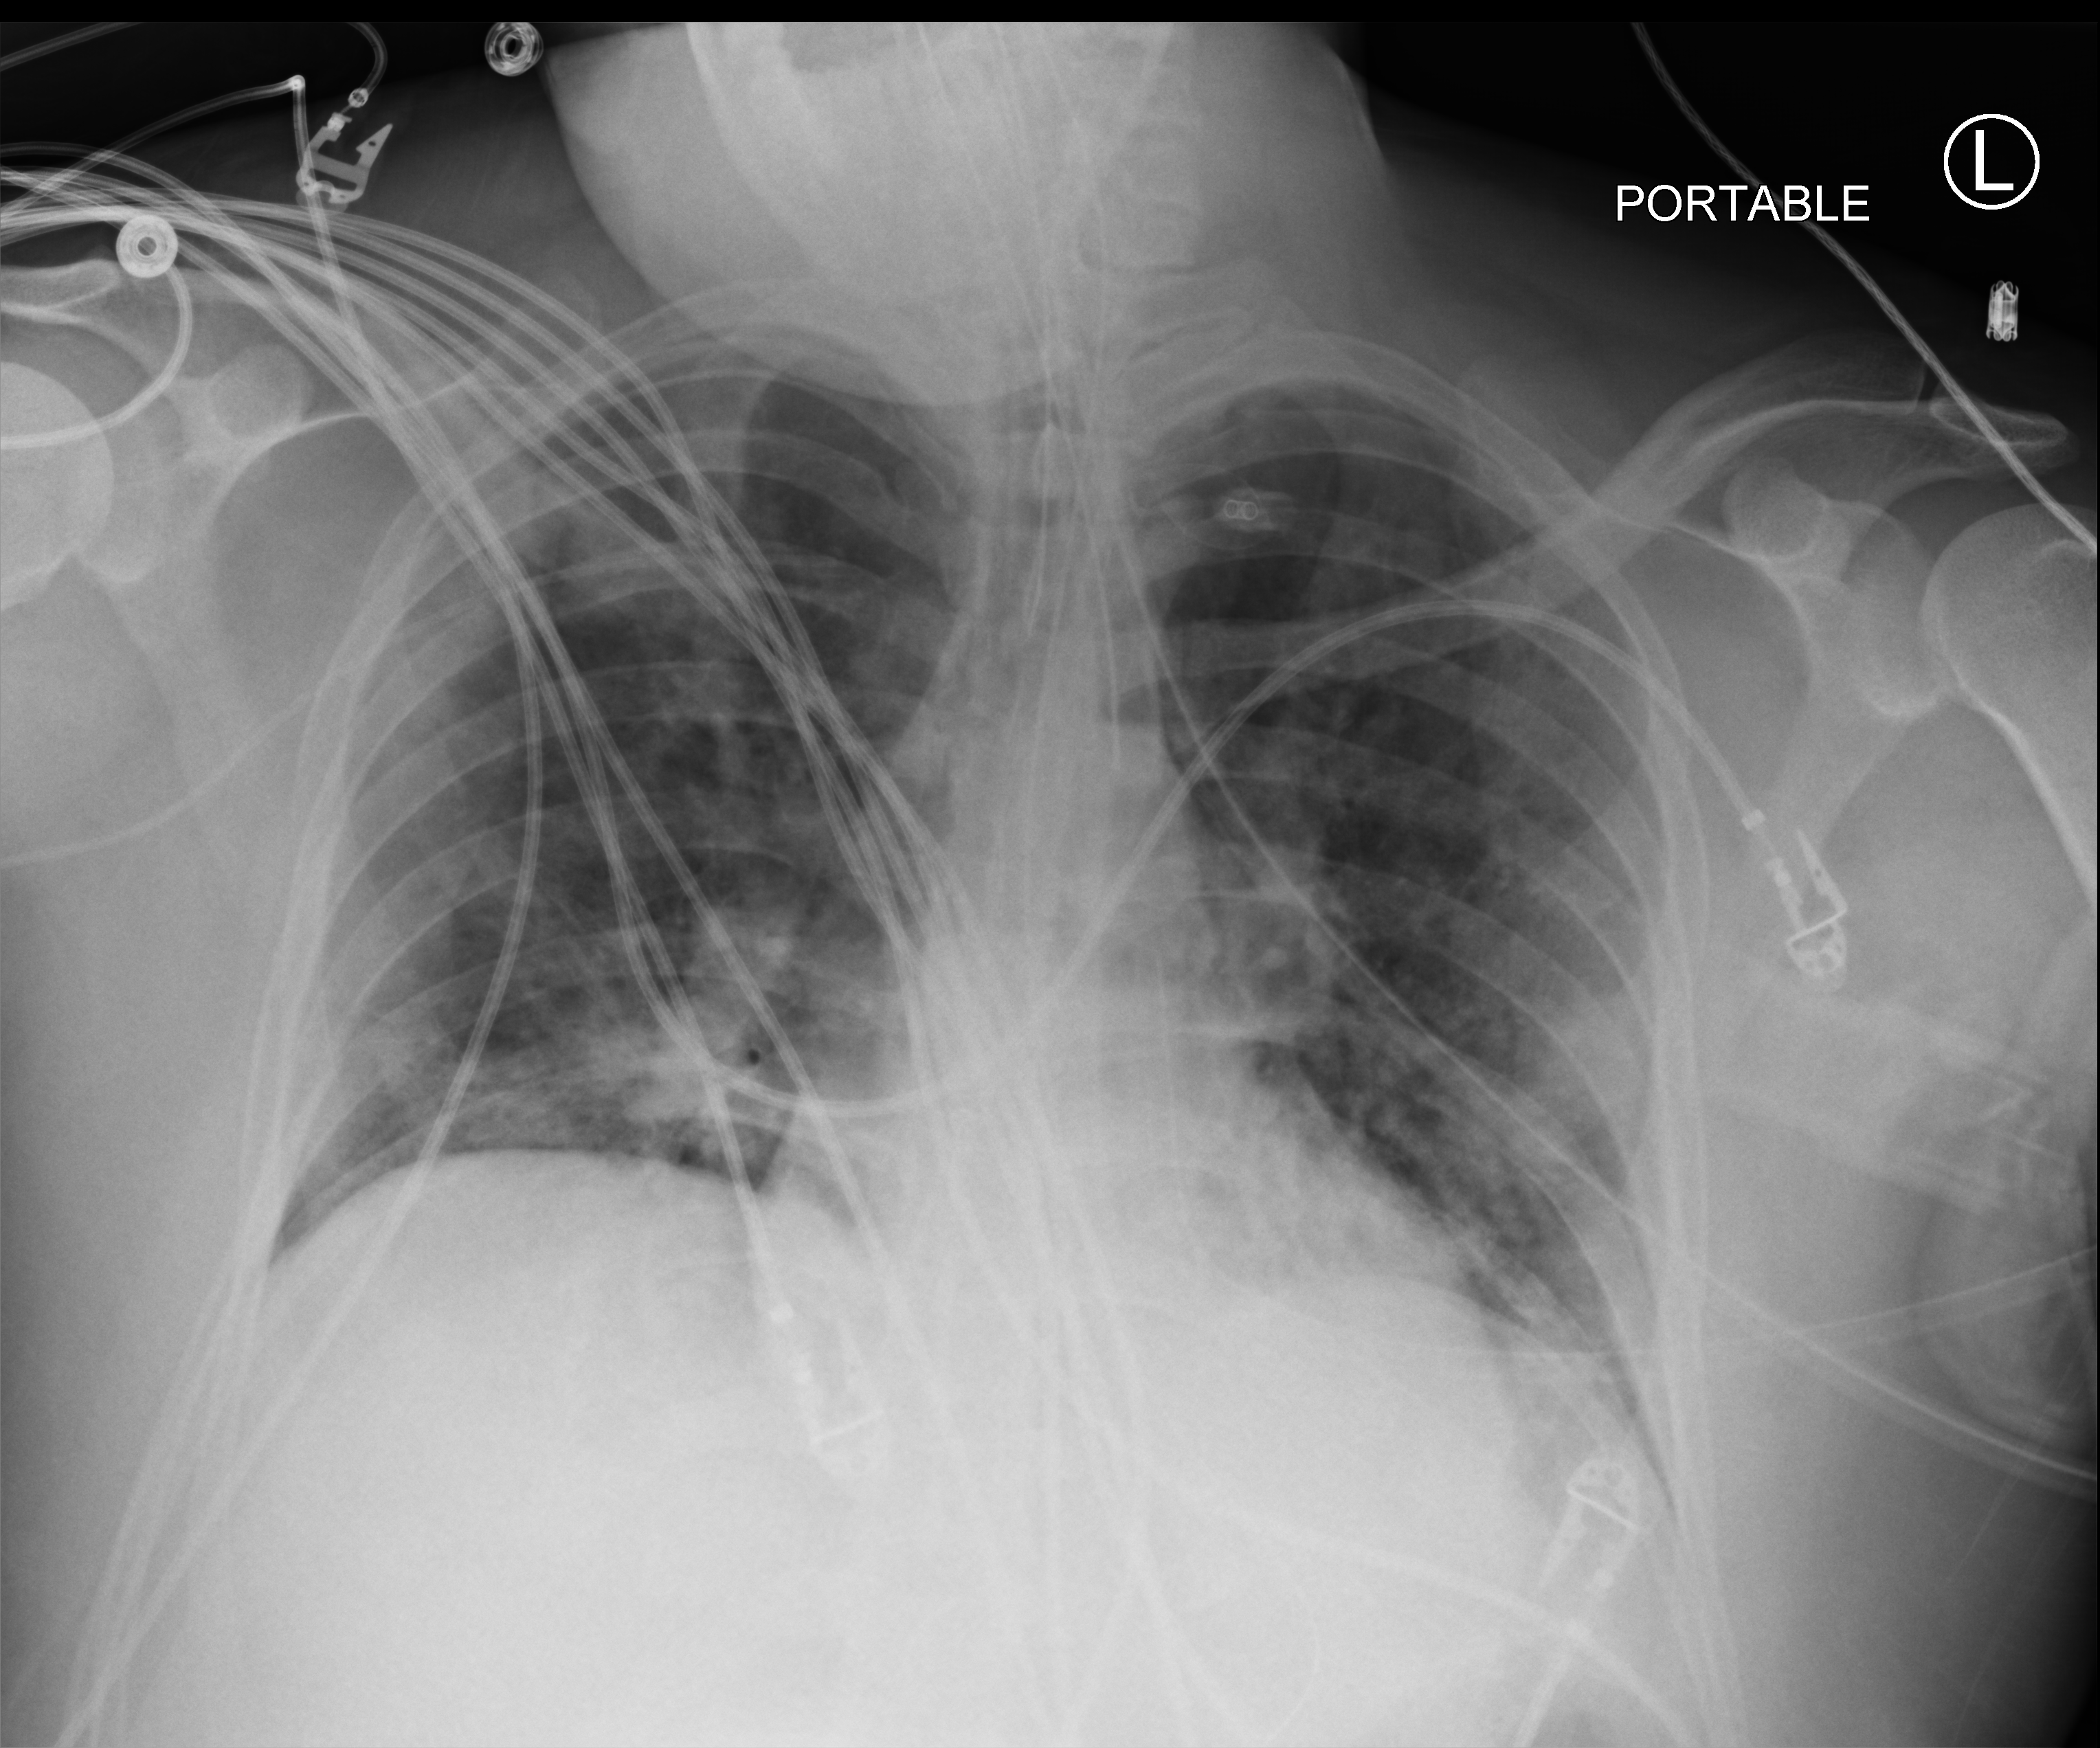
Portable chest radiograph; anteroposterior (AP) projection. Male patient hospitalised with COVID-19, age 18–59 years.
Hospital-stay facts (about this admission, not read from this image; timing relative to this image not recorded): smoking status (admission record): never; COPD (admission record): no; mechanically ventilated during this hospital stay: yes.